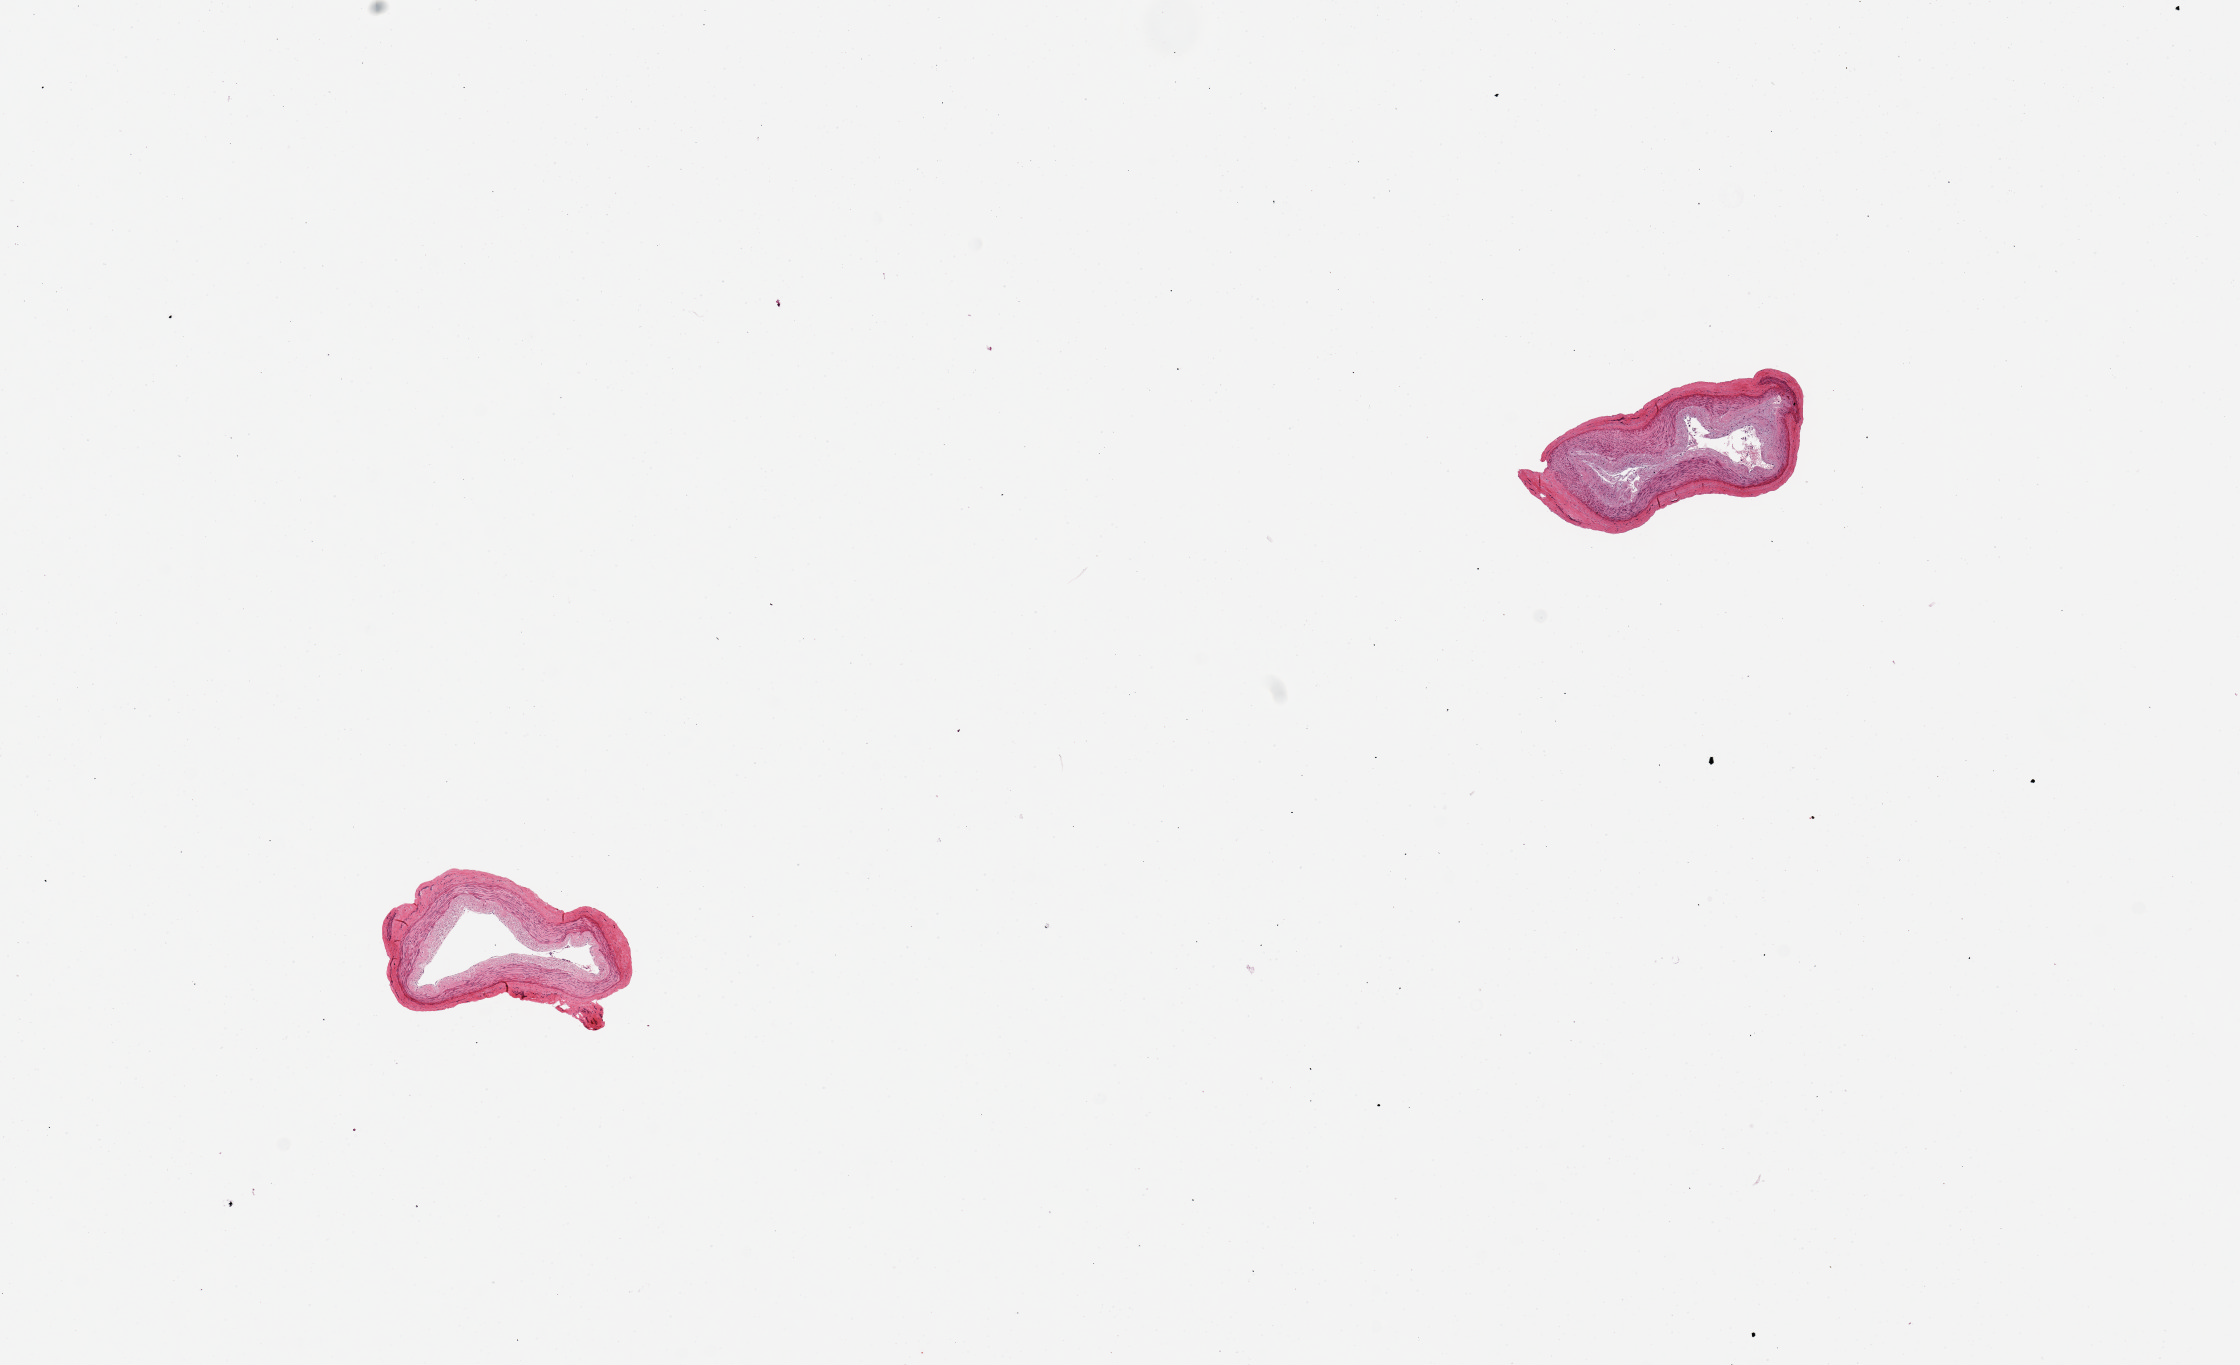
Whole-slide image, H&E stain, a low-resolution overview of the entire scanned area, about 17.7 x 10.8 mm (acquisition: 20x scan); PAXgene-fixed paraffin-embedded (PFPE) section; sampled site (target tissue): tibial artery; tissue donor sample. Female donor.
Reviewer comment on this tissue sample: 2 pieces, good clean specimens.